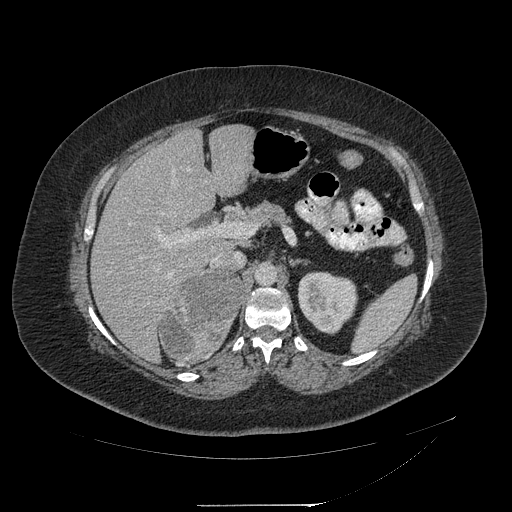
Contrast-enhanced abdominal CT, one axial slice. Position 130 of 217 along the scan axis. Reconstruction kernel STANDARD. 120 kVp. Intravenous contrast given. Soft-tissue window (W 400 / L 40 HU). 512 × 512 image matrix, field of view 453 × 453 mm. Patient: female, 55 years. From the clinical record (not read from this slice): diagnosis: adrenocortical carcinoma; tumour side: right adrenal; tumour size at pathology: 11 cm; Ki-67 index: 20 %; stage (as recorded): 2.
Structures marked on this image (semi-automatic segmentation, software-assisted and operator-edited):
- mass: box from (x=159, y=273) to (x=242, y=361) px